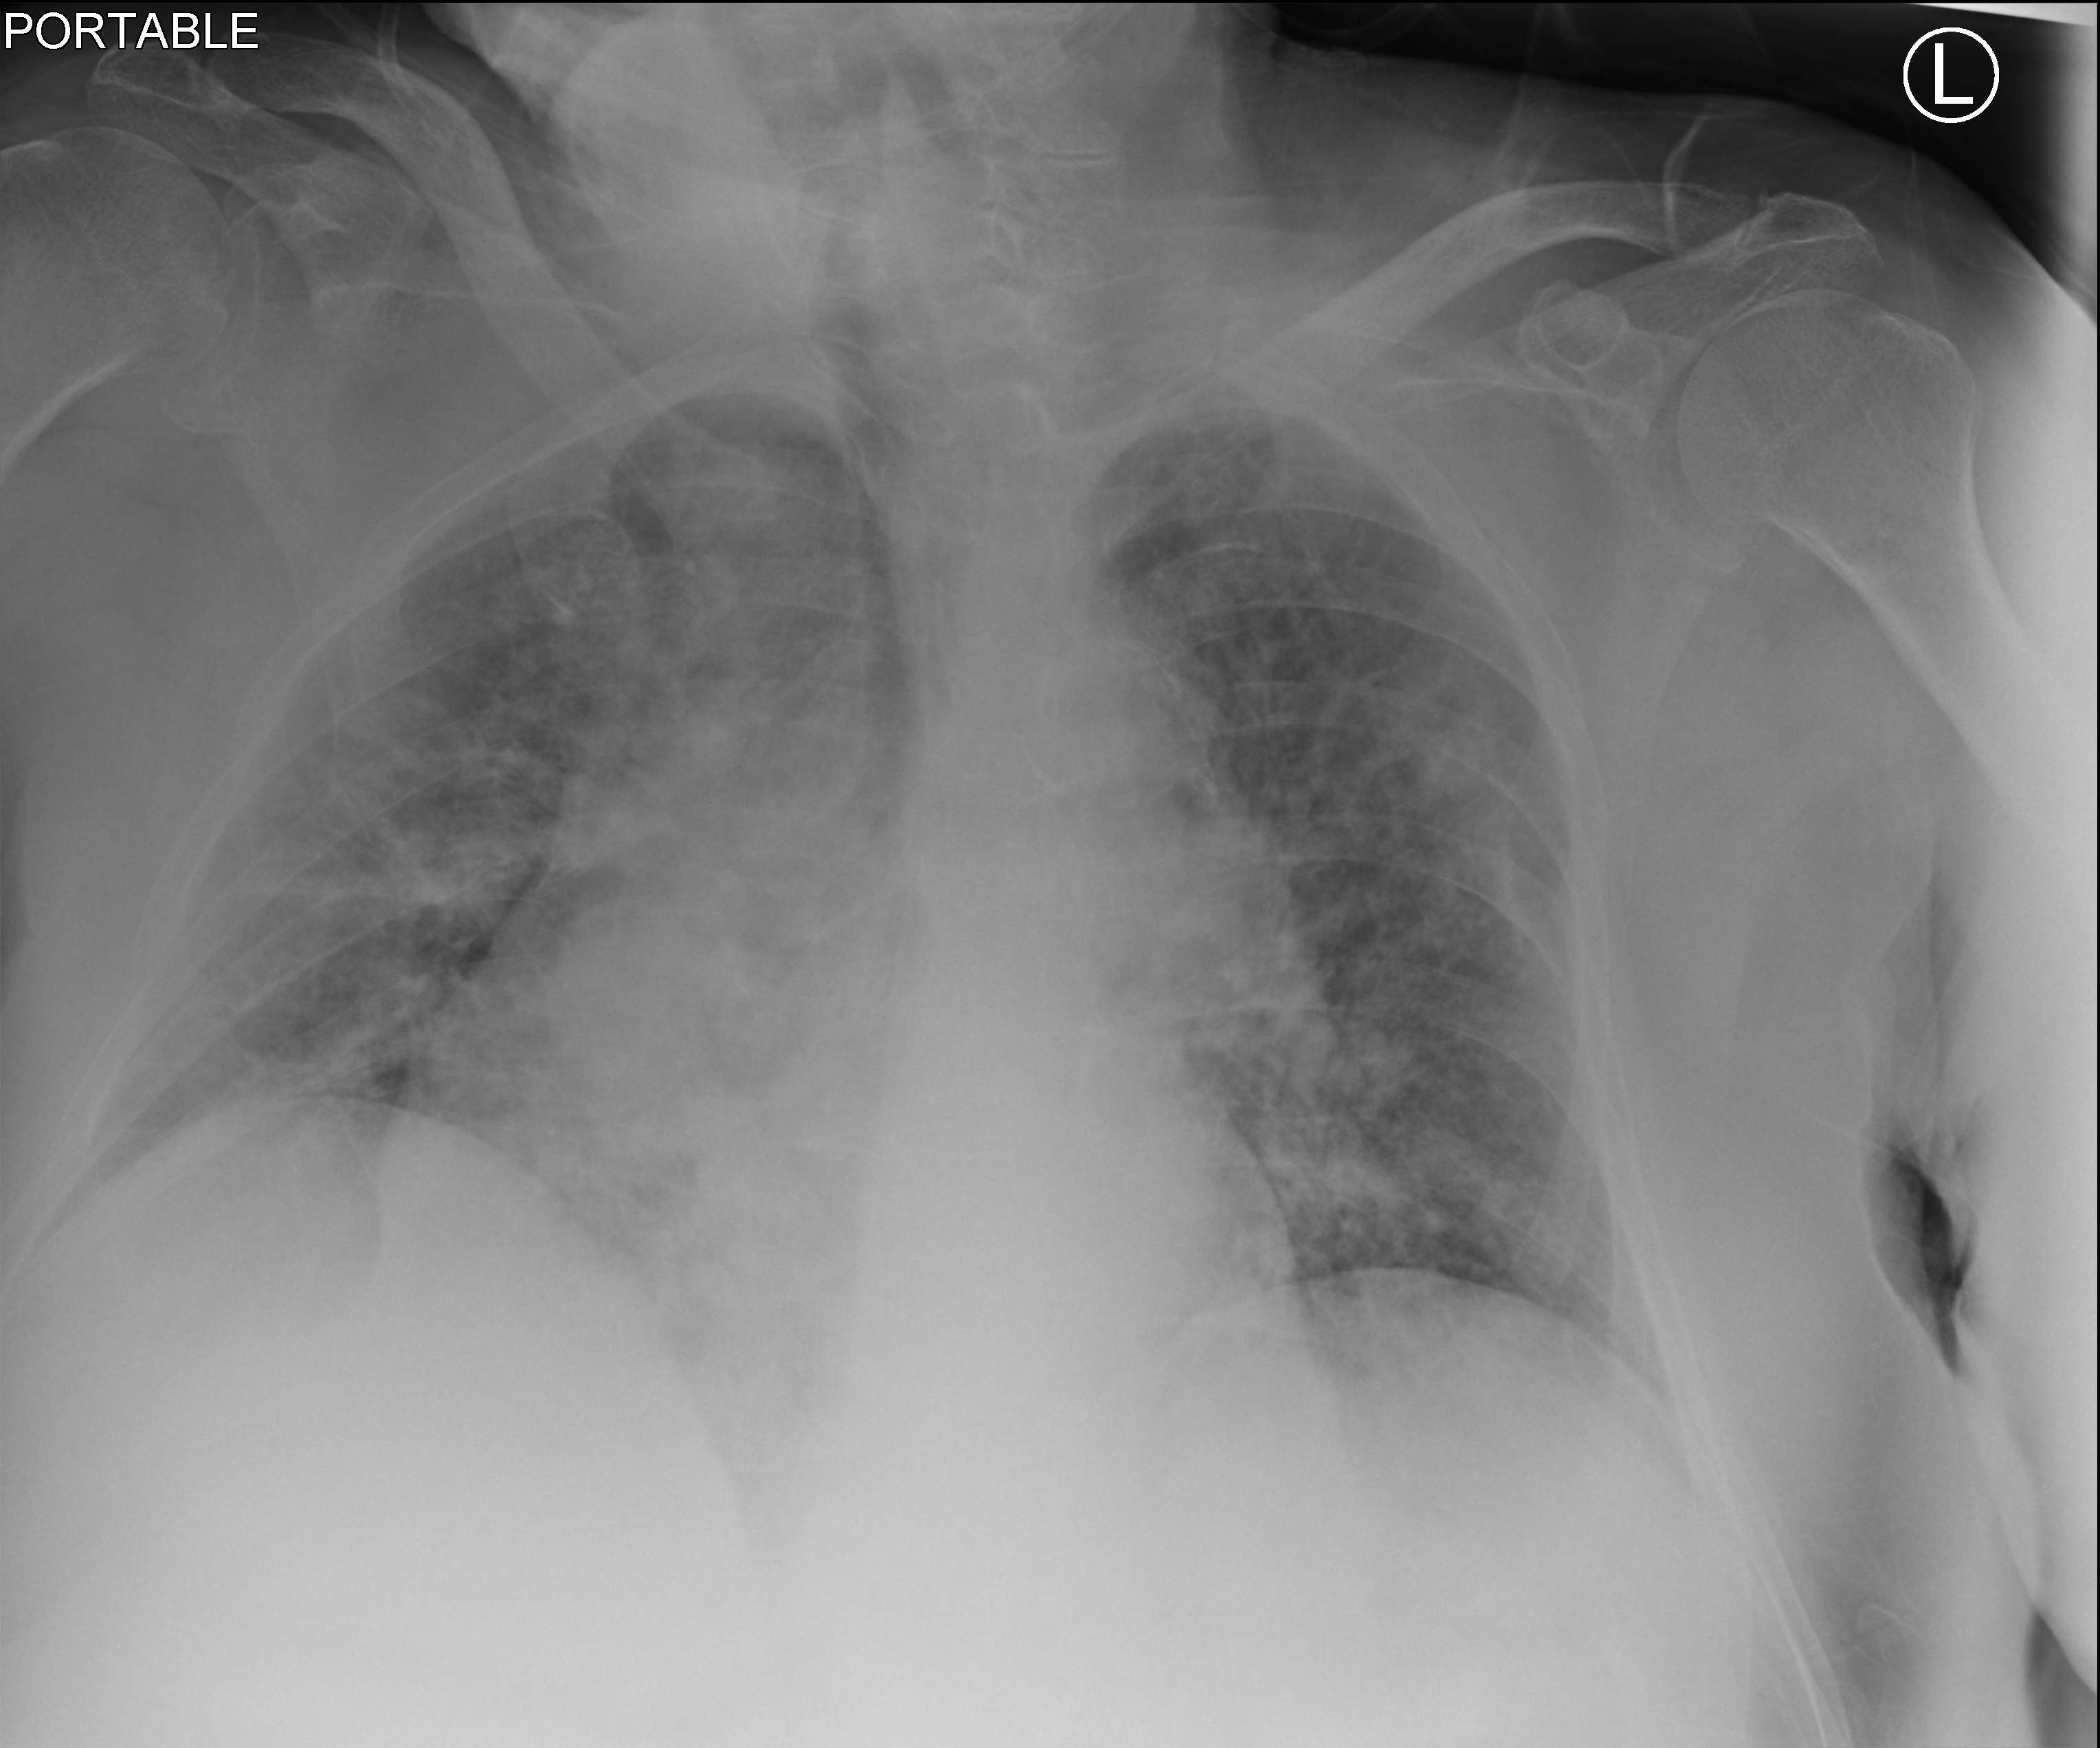
Chest X-ray (portable). Male patient hospitalised with COVID-19, age 75–90 years.
Admission-level facts for this patient (not findings on this image; timing relative to this image not recorded): mechanically ventilated during this hospital stay: no; admitted to intensive care during this hospital stay: no.